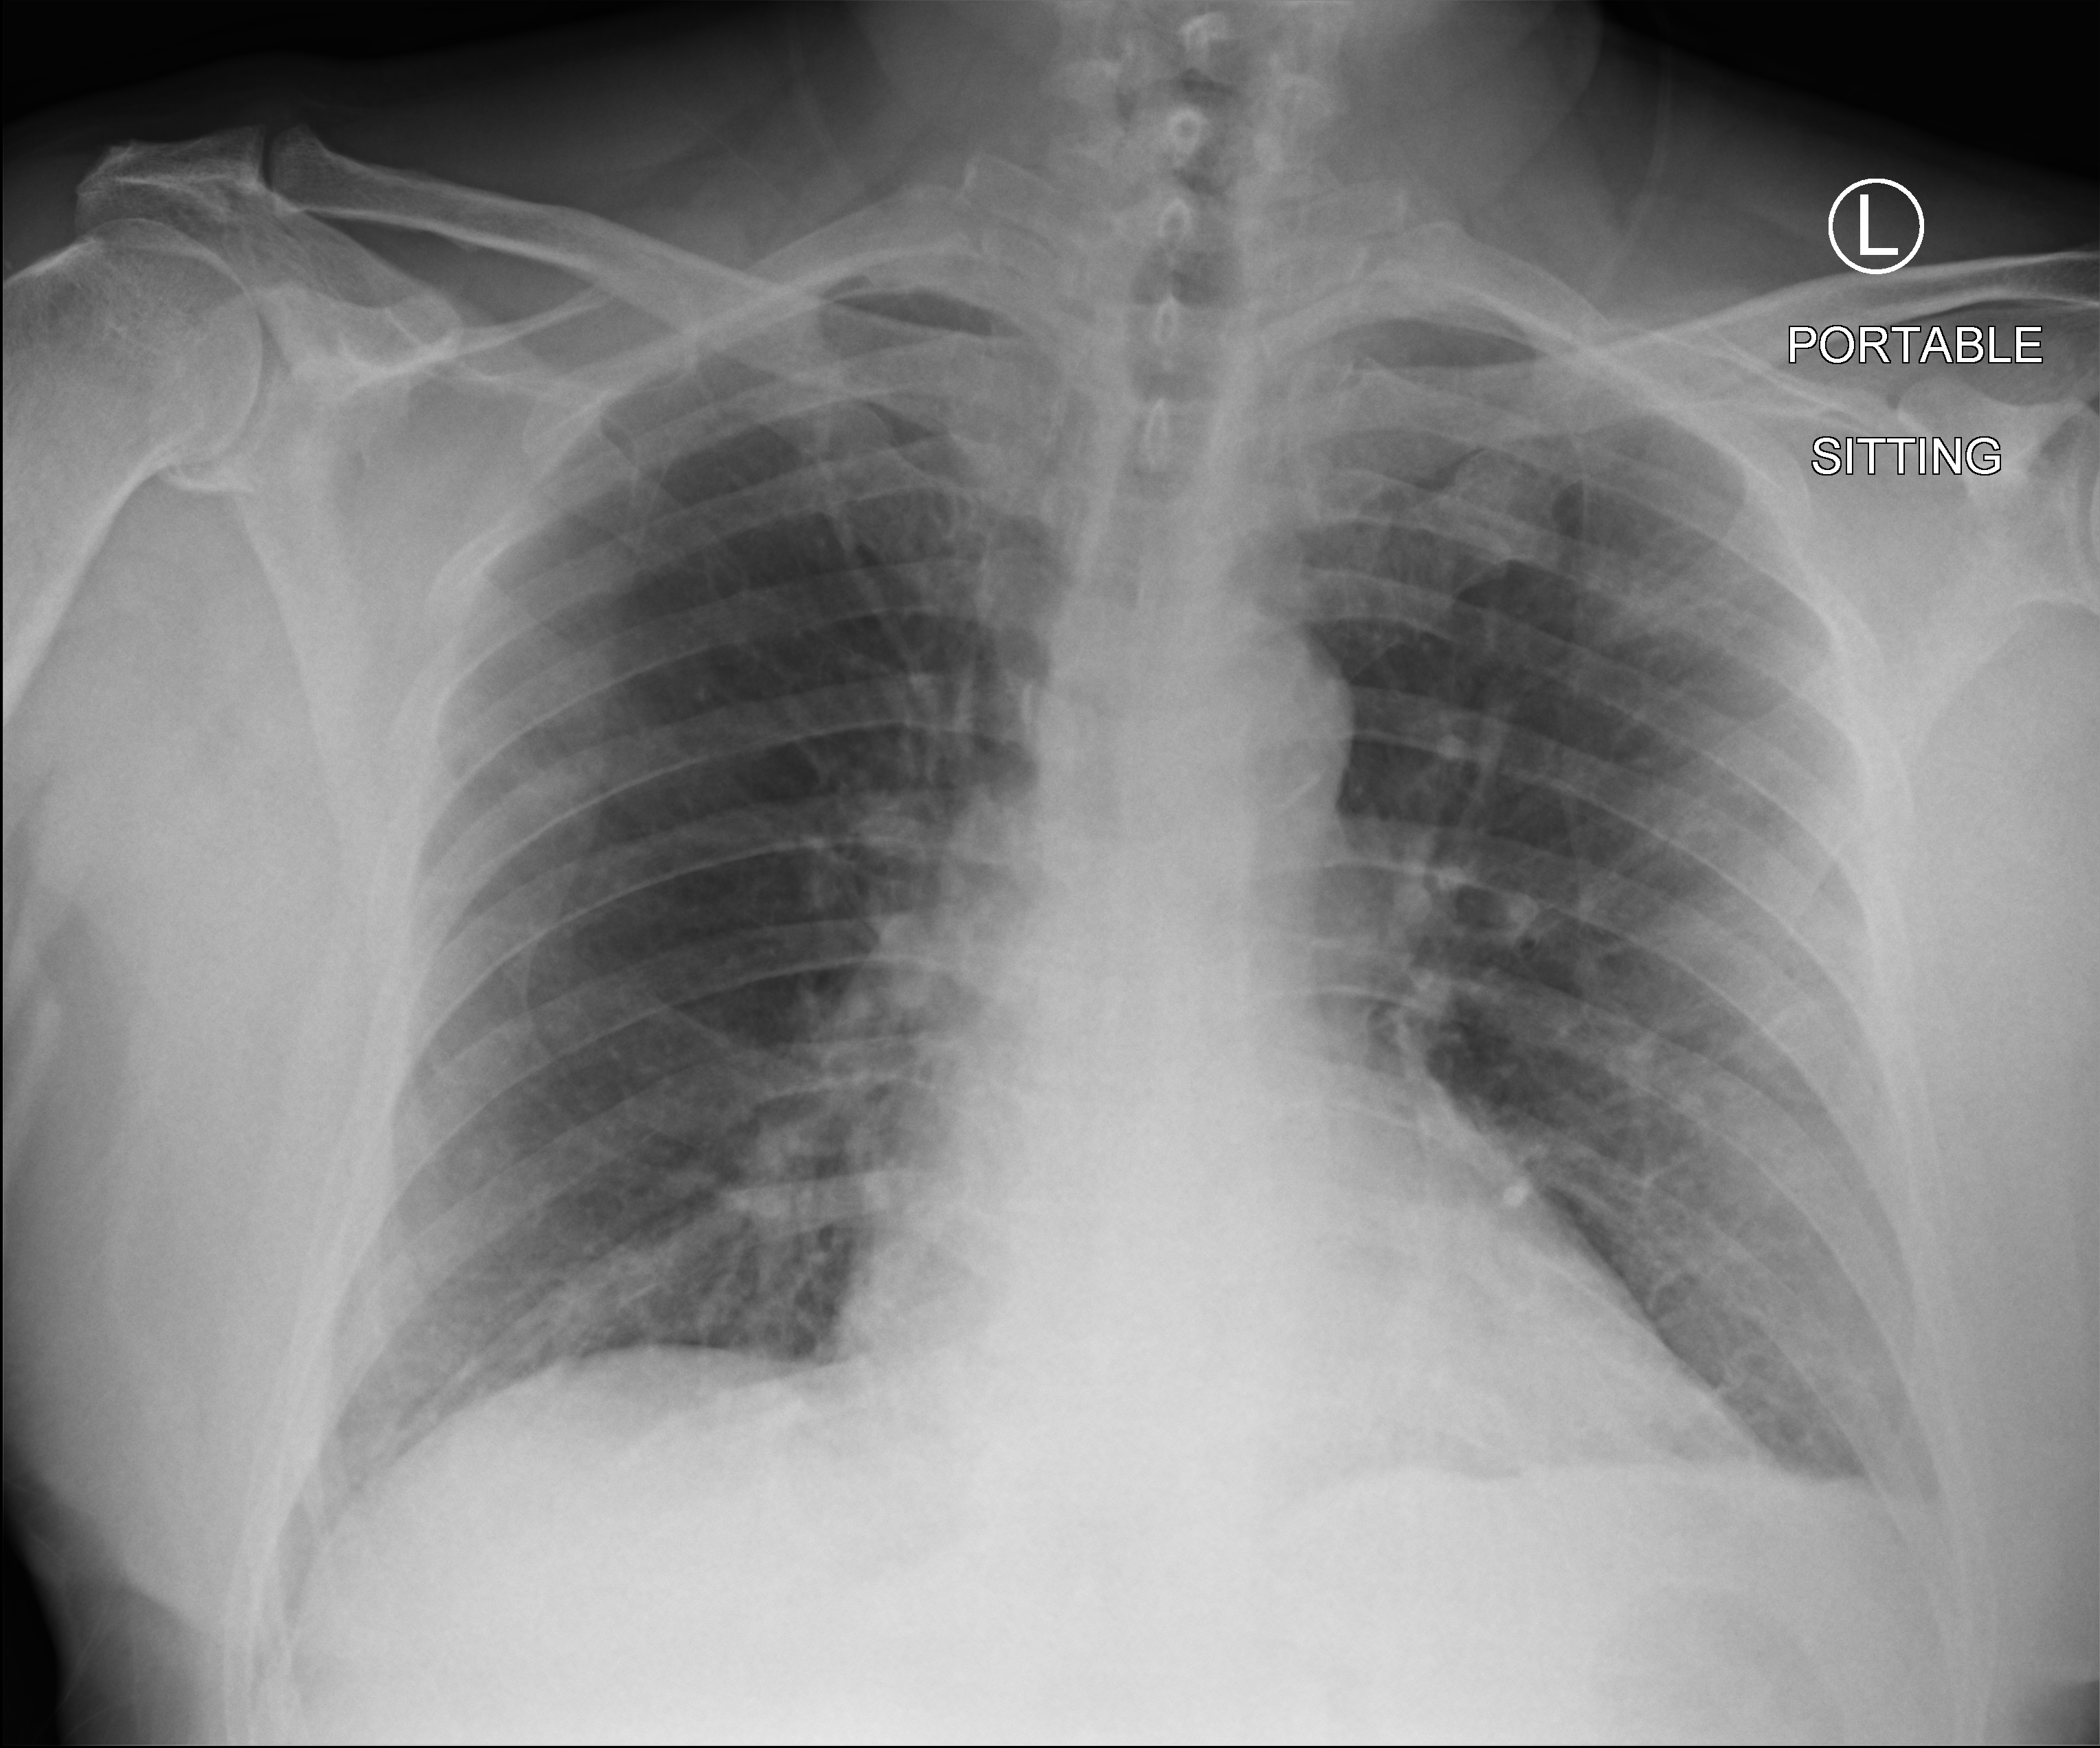
Bedside chest radiograph (computed radiography); anteroposterior (AP) projection. Patient hospitalised with COVID-19; male, aged 60–74 years.
Admission-level facts for this patient (not findings on this image; timing relative to this image not recorded): admitted to intensive care during this hospital stay: no.